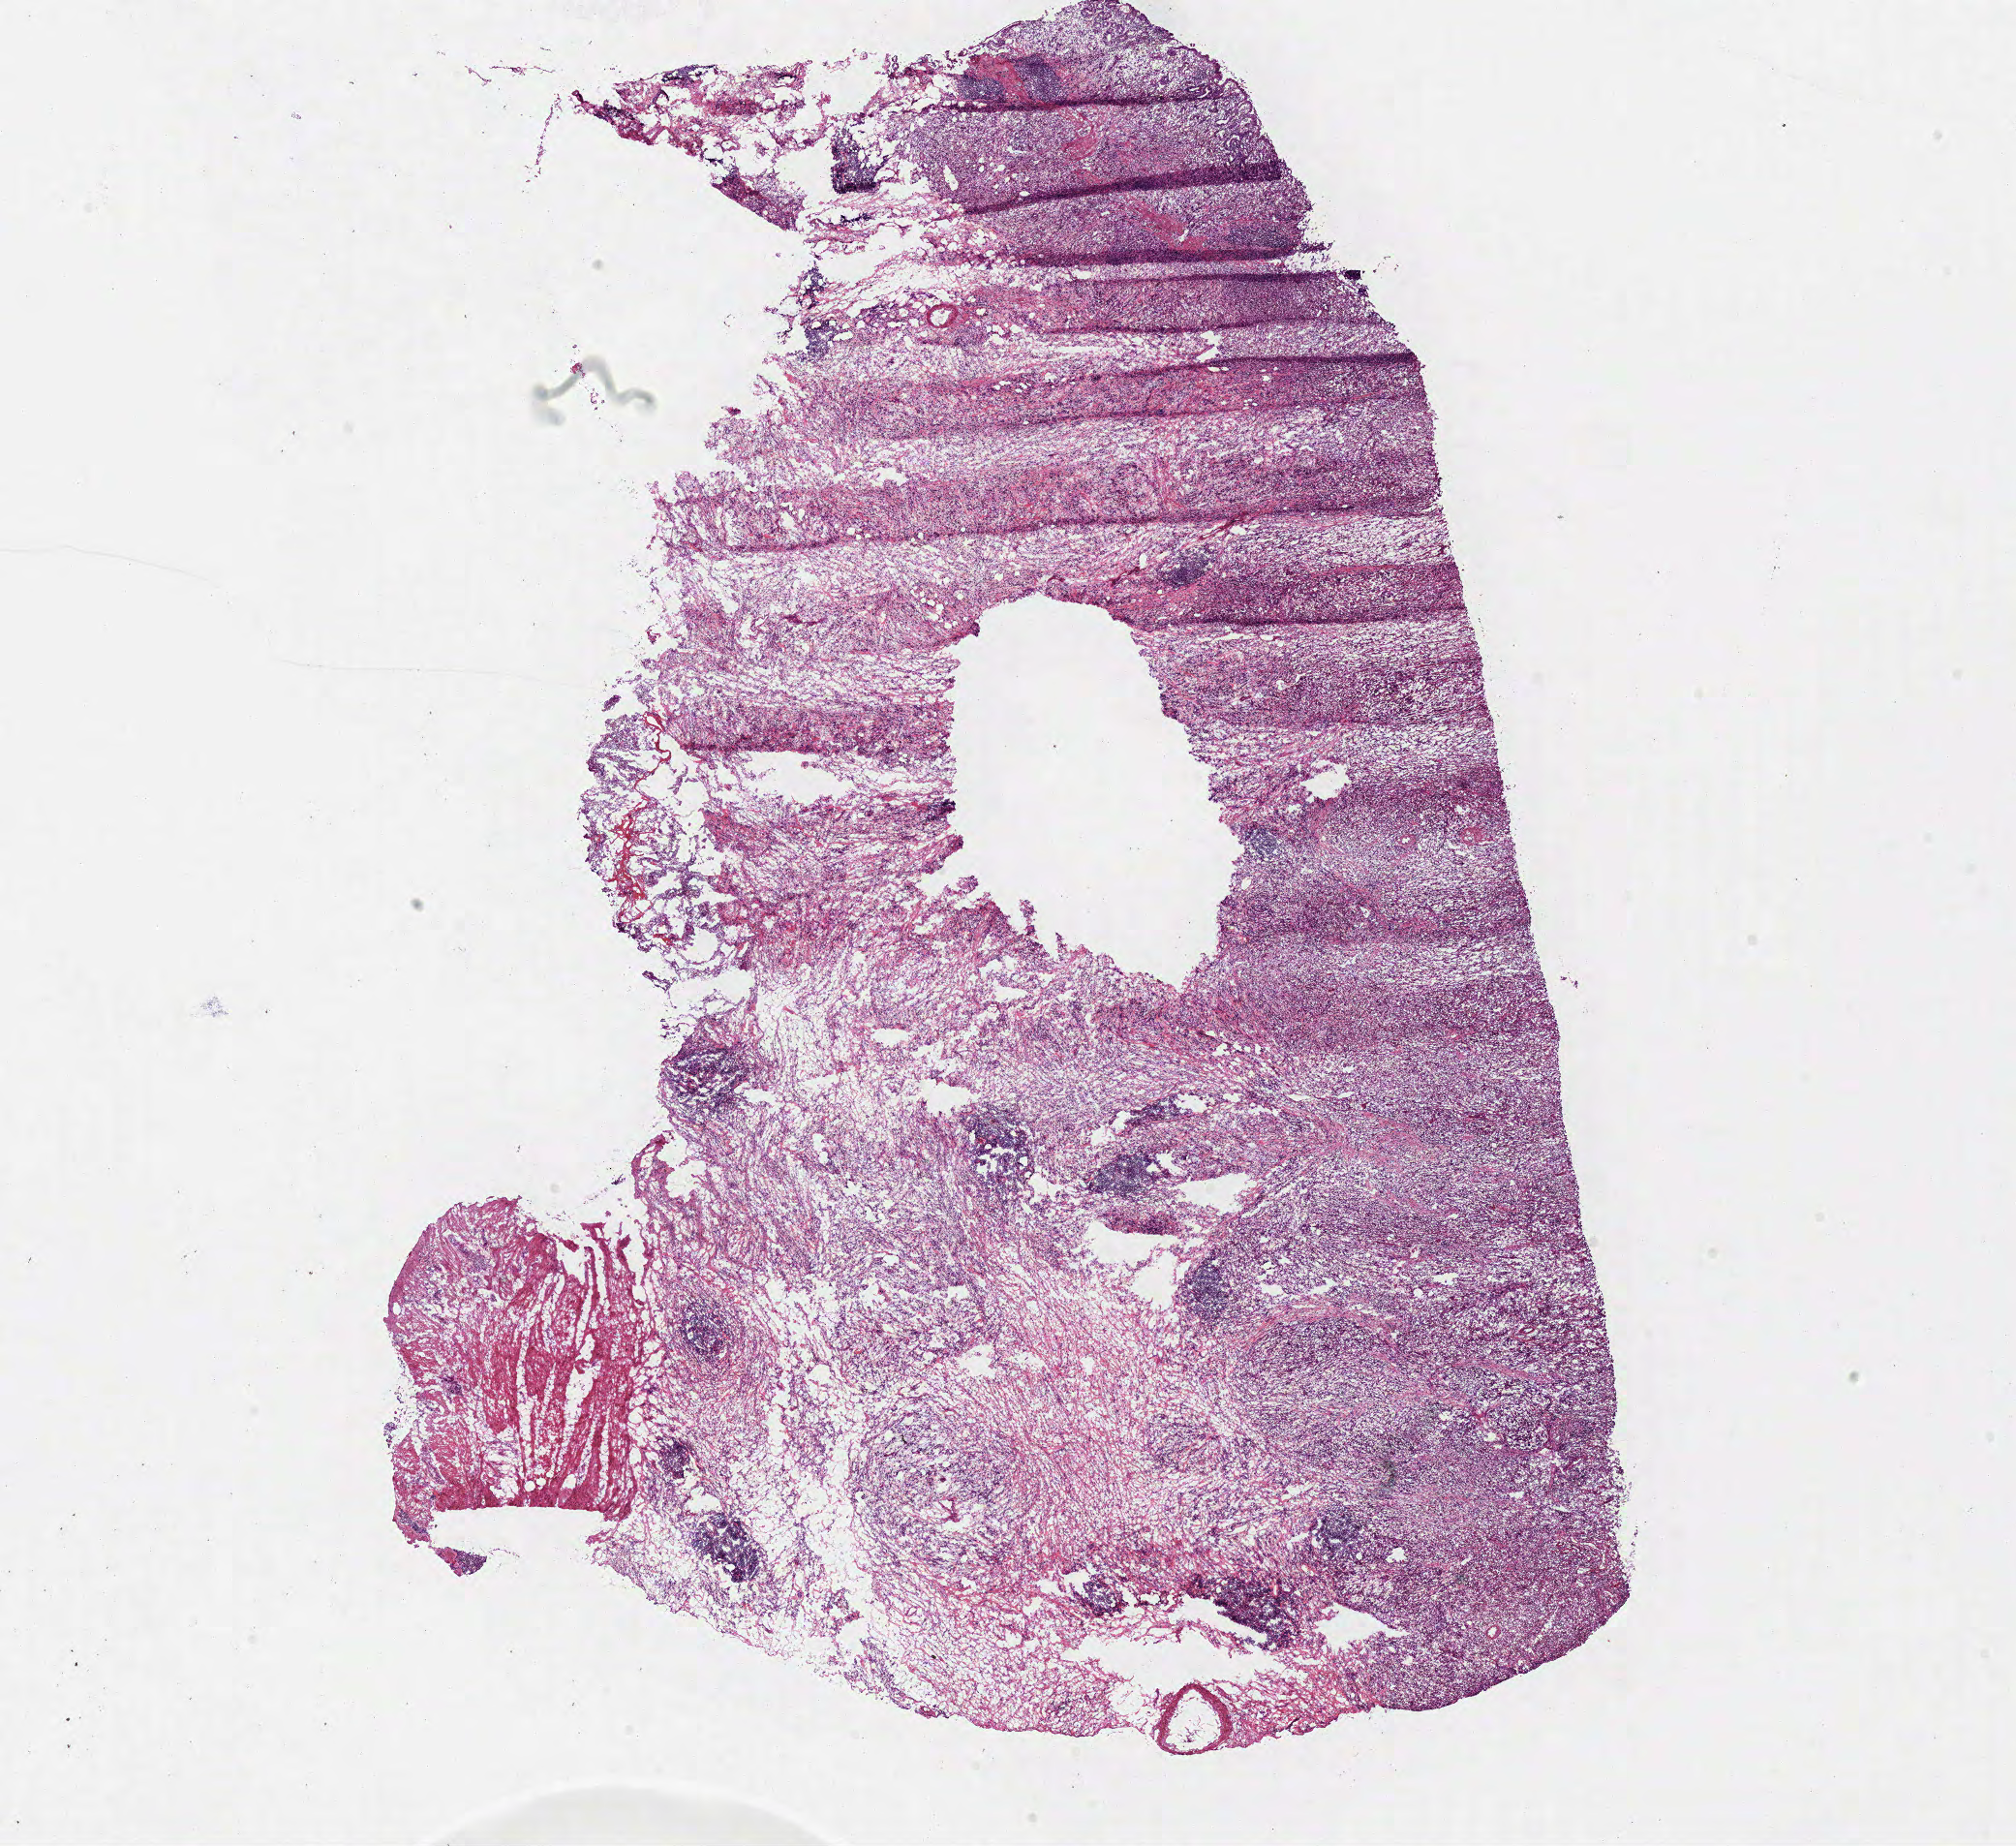
H&E-stained whole-slide image — shown as a low-resolution overview of the whole scanned area (about 16.4 x 15.0 mm). Frozen section from the bottom of the tissue portion. Sample: primary tumour, stomach. Patient: male, age at initial diagnosis 54 years. Histologic grade: G3 (poorly differentiated). Slide review estimates, as recorded: tumour cells 85%, tumour nuclei 70%, normal cells 8%, stromal cells 7%, necrosis 0%. Inflammatory infiltration, as recorded: lymphocyte infiltration 10%, monocyte infiltration 0%, neutrophil infiltration 10%.
* histologic diagnosis: Adenocarcinoma, NOS (body of stomach)
* lymph nodes positive (case pathology): 1 of 2 examined
* TNM: T2 N1 M0
* AJCC pathologic stage: IIA